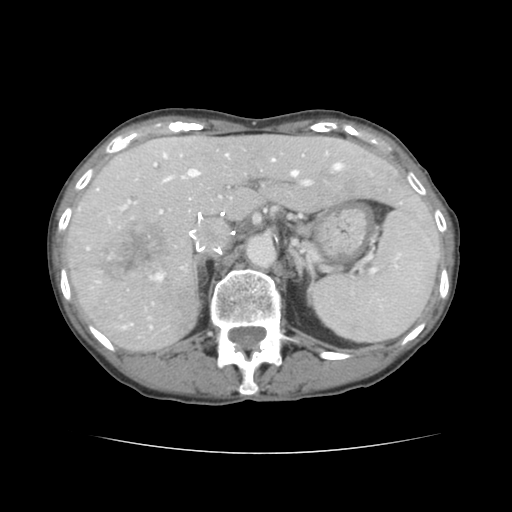
Contrast-enhanced abdominal CT, one axial slice. Slice 94 of 136 in the series (ordered by position). Soft-tissue window (W 400 / L 40 HU). 512 × 512 image matrix, field of view 319 × 319 mm. Female patient, age 77 years. Case-level facts recorded for this patient, not image findings: diagnosis: colorectal cancer liver metastases, imaged before liver resection; multiple liver metastases: yes; largest metastasis: 3 cm.
Annotated regions visible in this slice (expert manual segmentation):
- hepatic veins: box from (x=122, y=154) to (x=342, y=329) px
- liver: (x=68, y=136)–(x=429, y=352)
- planned liver remnant (the part of the liver to remain after resection): (x=153, y=136)–(x=430, y=224)
- portal vein (with intrahepatic branches): (x=97, y=163)–(x=314, y=280)
- liver metastasis: (x=97, y=220)–(x=172, y=283)